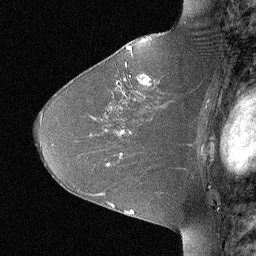
Breast MRI (dynamic contrast-enhanced), one sagittal slice. Position 43 of 64 along the scan axis. Dynamic contrast-enhanced study with each time point stored as its own series, time point 2 of 3 at this slice position (early post-contrast, ordered by acquisition time). 1.5 T. TE 4 ms, TR 30 ms. 256 × 256 image matrix, field of view 180 × 180 mm. Female patient, age 46 years. Case-level facts recorded for this patient, not image findings: setting: breast cancer imaged before/during neoadjuvant chemotherapy; receptor status: HR-positive, HER2-negative.
Annotated regions visible in this slice (semi-automatic segmentation, software-assisted and operator-edited):
- analysis volume of interest (the breast-tissue region the enhancement analysis was run in; not a lesion): bounding box [x1, y1, x2, y2] px = [106, 43, 184, 119]
- tumour enhancement mask (voxels above the 90 % enhancement threshold inside the analysis volume of interest): [126, 47, 132, 49]